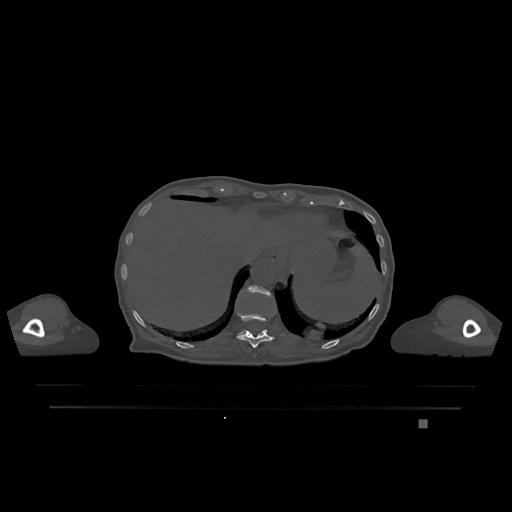
CT including the spine, one axial slice. Position 576 of 1317 along the scan axis. Bone window (W 1800 / L 400 HU). 0.5 mm slice thickness. 512 × 512 image matrix, field of view 500 × 500 mm. Patient: female, 74 years. From the clinical record (not read from this slice): primary cancer: lung; vertebrae with lytic lesions (as recorded): T1, T4, T5, T6, L4, L5.
Structures marked on this image (semi-automatically segmented with operator editing):
- T11 vertebra: bounding box (x1, y1, x2, y2) in pixels: (237, 312, 275, 348)
- T12 vertebra: (241, 285, 271, 334)